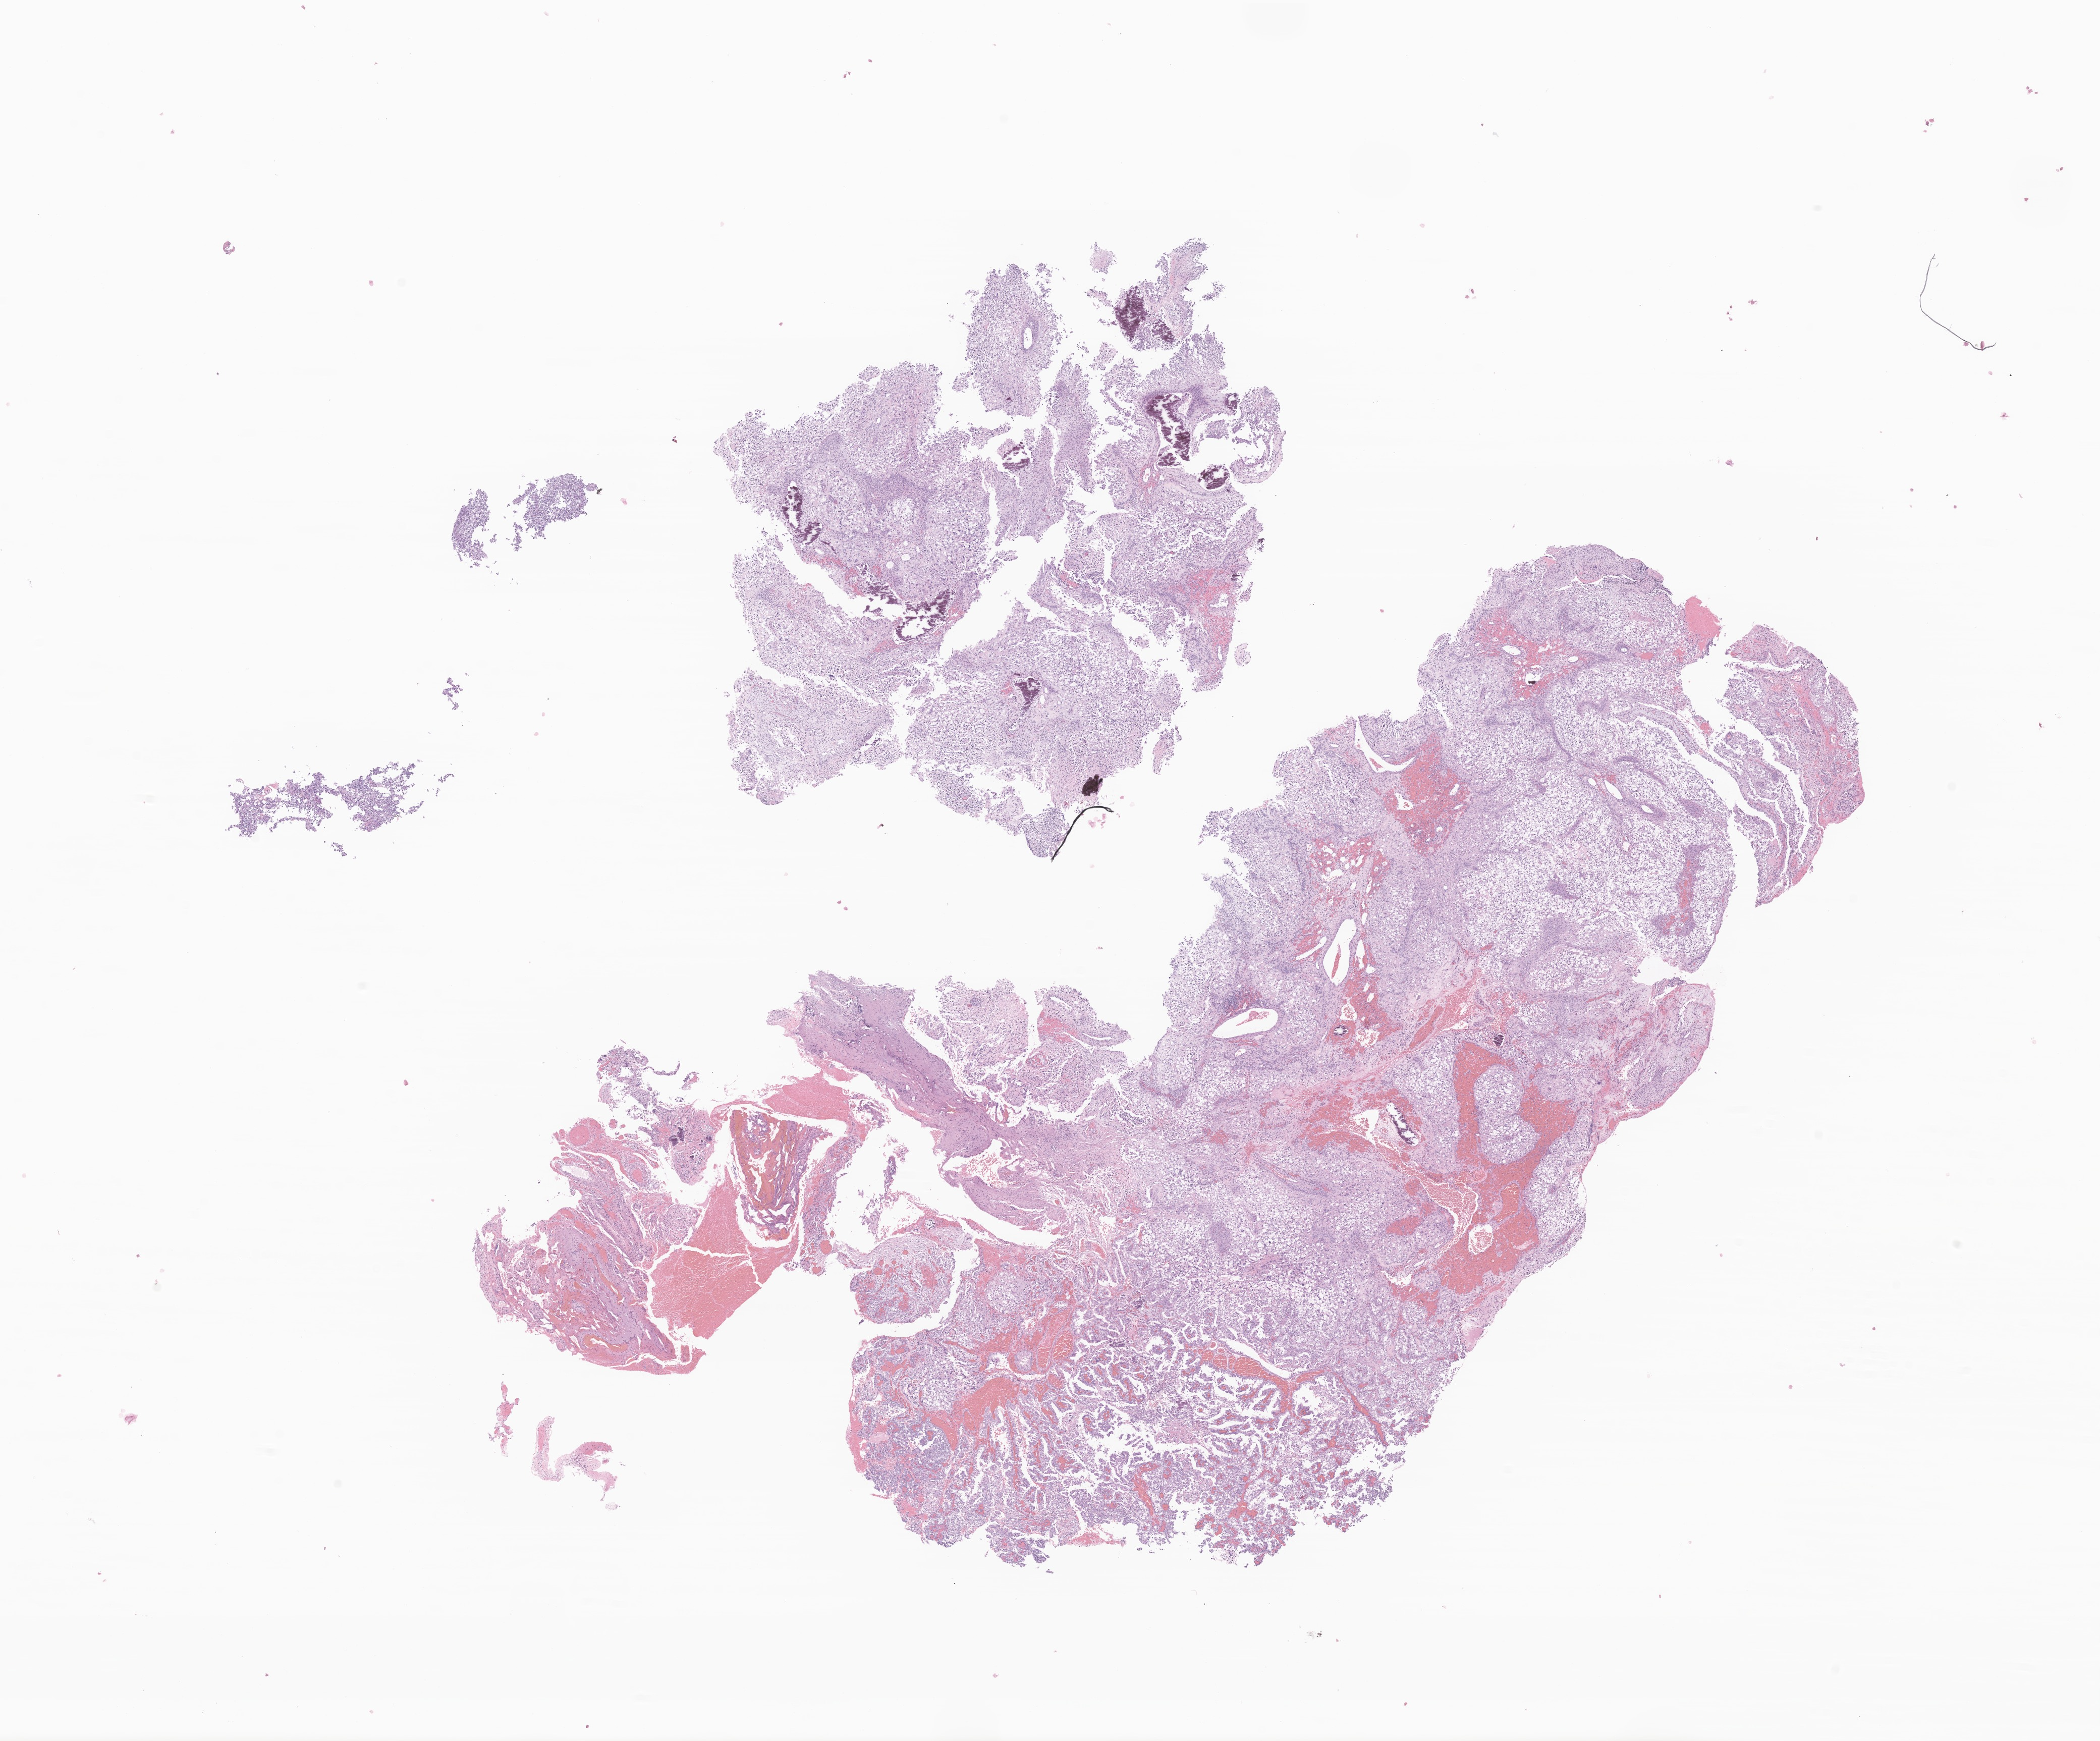
Digitized H&E-stained section of tumor tissue from the choroid of eye, low-resolution overview of the scanned area, about 17.5 x 14.5 mm, FFPE section. Male patient, age 172 days.
Recorded diagnosis: Choroid plexus carcinoma.